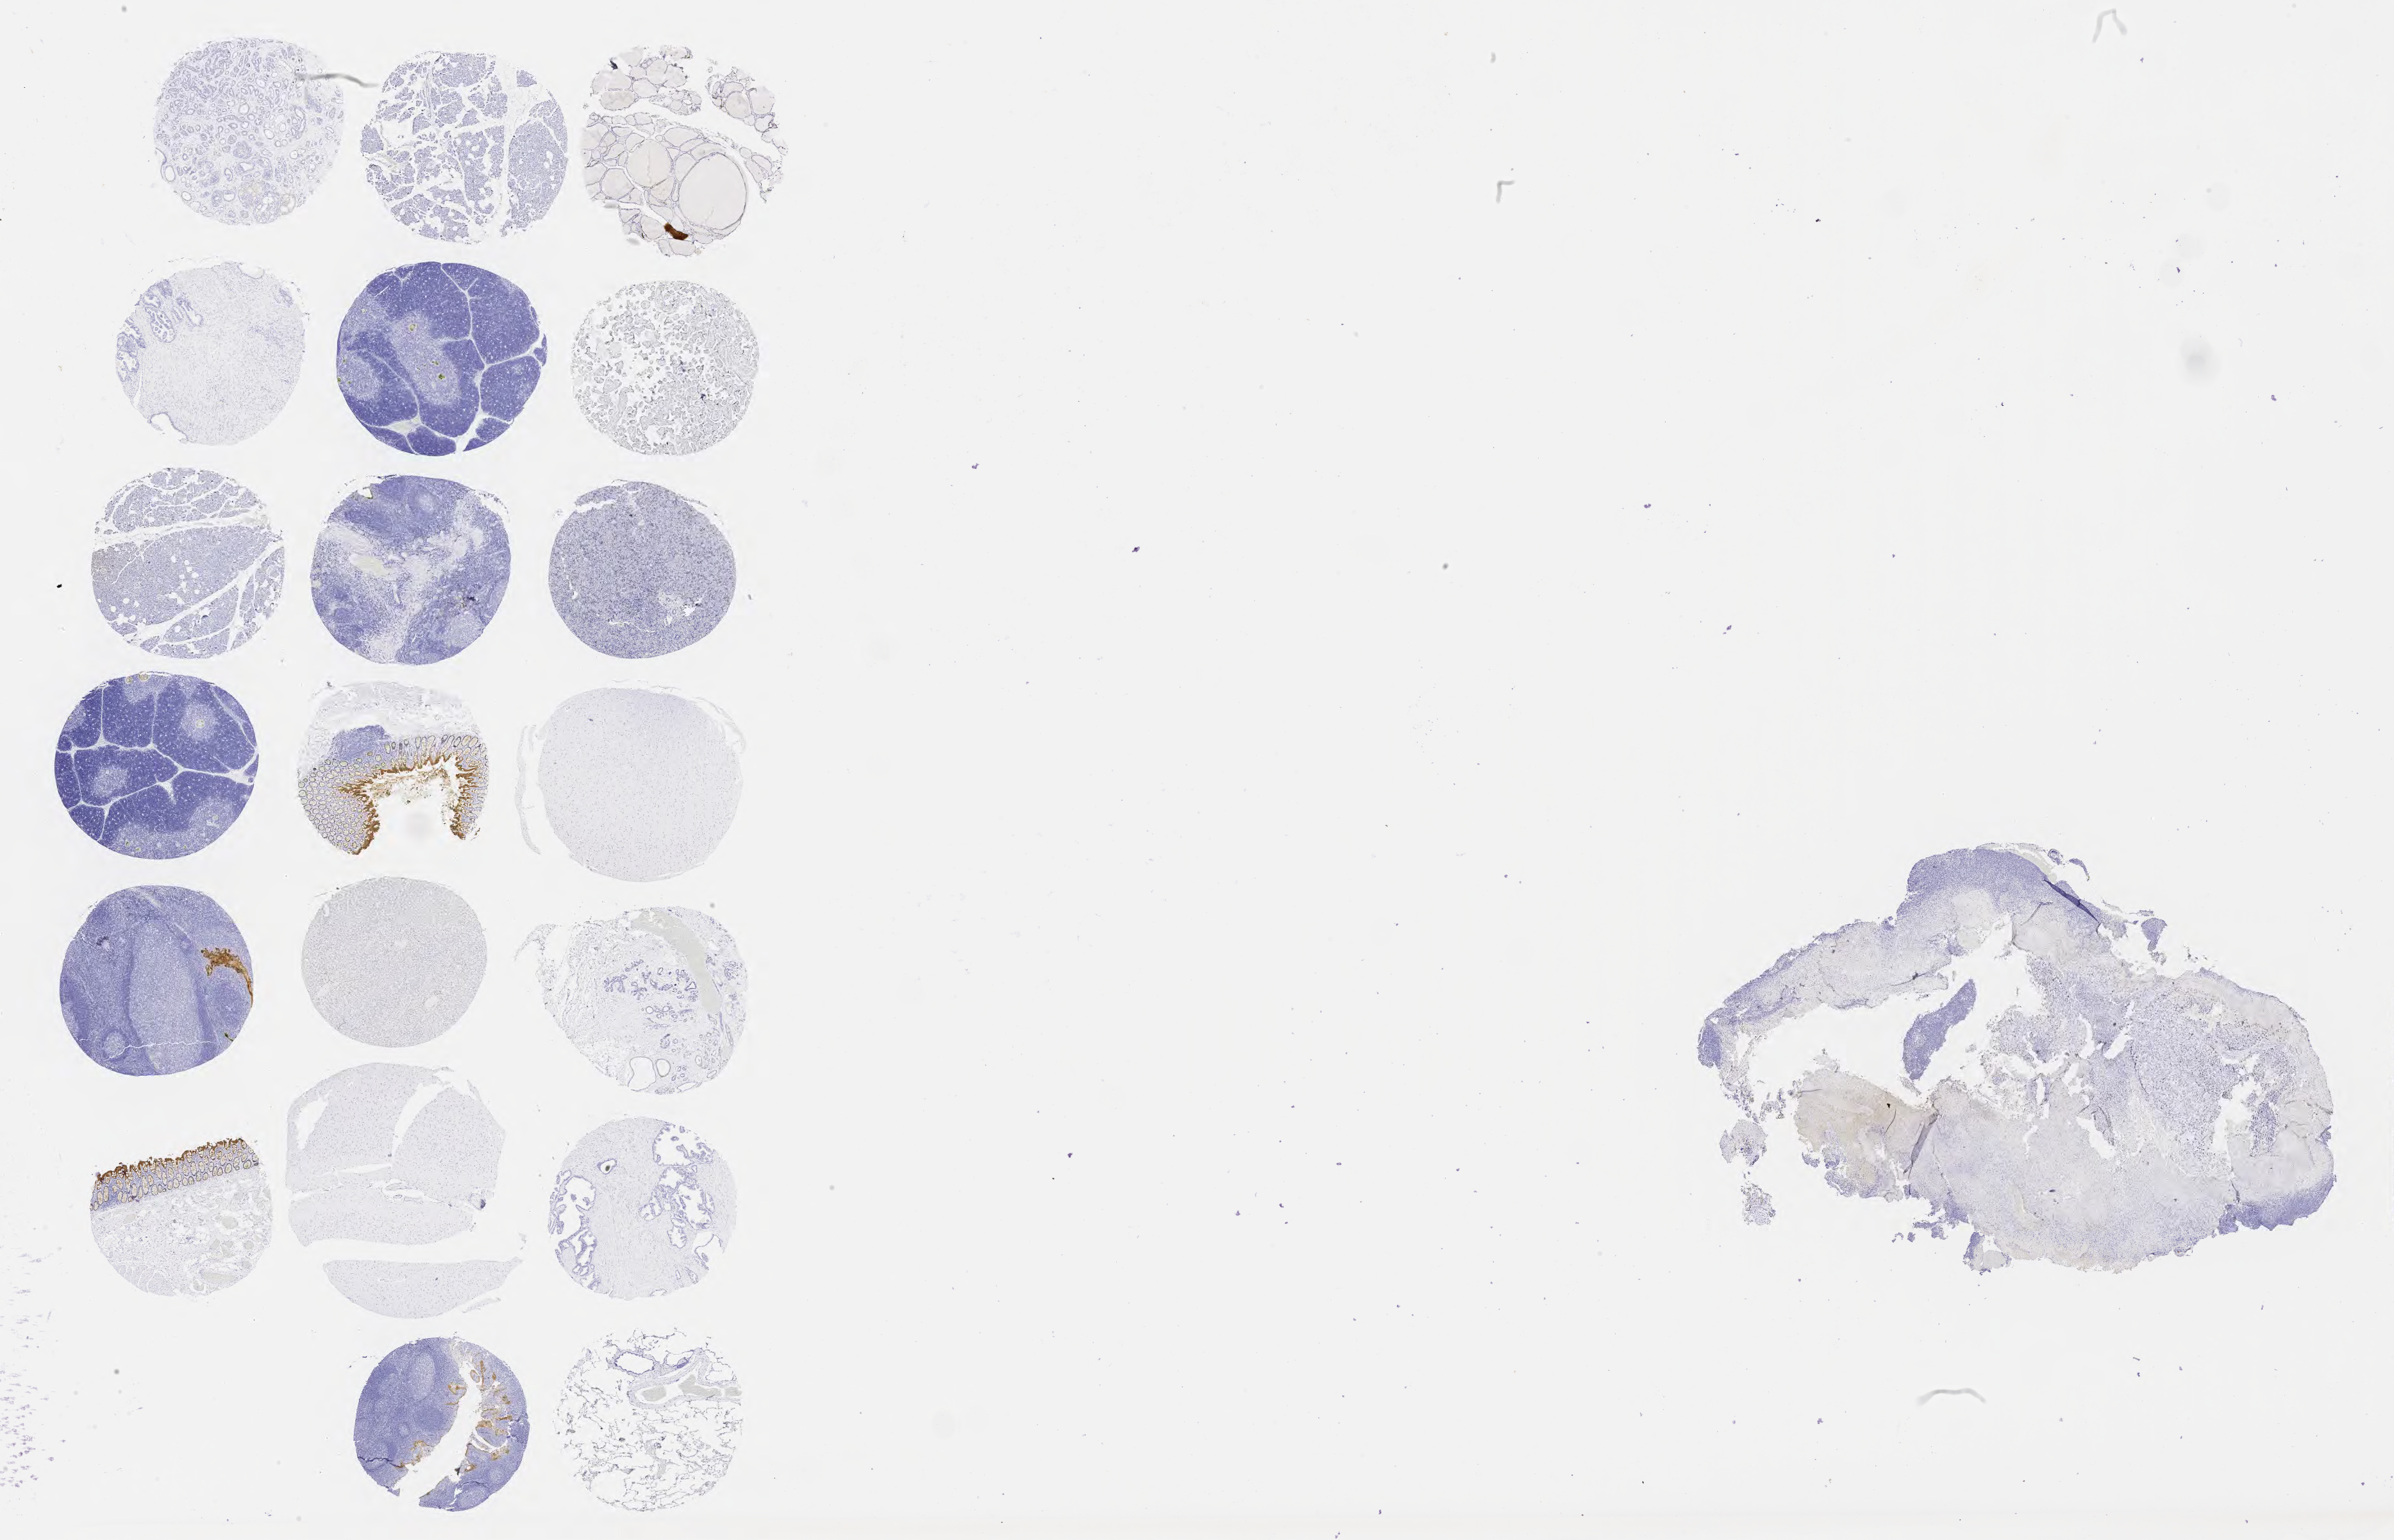
IHC for carcinoembryonic antigen (CEA), whole-slide image — shown as a low-resolution overview of the whole scanned area (about 30.2 x 19.4 mm). Specimen: tumor tissue. Site: cervix. Patient female; age 62 years.
- histologic diagnosis: Squamous cell carcinoma, large cell, nonkeratinizing, NOS